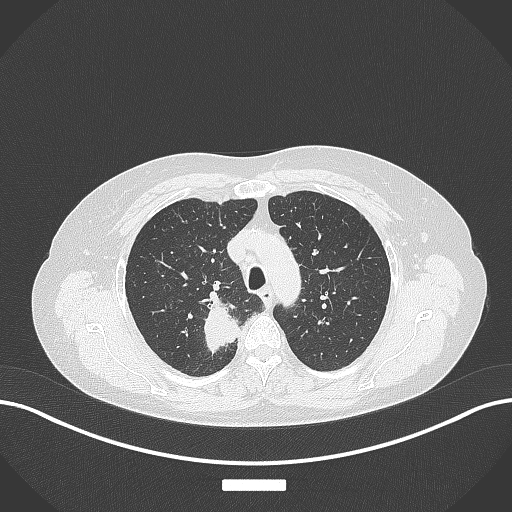
Chest CT, one axial slice; slice 291 of 357 in the series (ordered by position); reconstruction kernel B70f; lung window (W 1500 / L -600 HU); 1 mm slice thickness; 512 × 512 image matrix, field of view 400 × 400 mm. Female patient, age 62 years. Case-level facts recorded for this patient, not image findings: clinical TNM (as recorded): T1c N1 M0.
Annotated regions visible in this slice (bounding box drawn by a radiologist):
- lung tumour (recorded histology: squamous cell carcinoma): bounding box (x1, y1, x2, y2) in pixels: (195, 297, 234, 357)